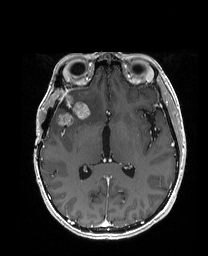
Brain MRI from a brain-tumour surgery series, one axial slice. Position 94 of 192 along the scan axis. T1-weighted post-contrast. 208 × 256 image matrix. Case-level facts recorded for this patient, not image findings: histopathology: Metastatic Carcinoma from Breast primary.
Annotated regions visible in this slice (expert manual segmentation):
- previous resection cavity: bounding box (x1, y1, x2, y2) in pixels: (60, 102, 70, 112)
- tumour: (55, 94, 104, 125)